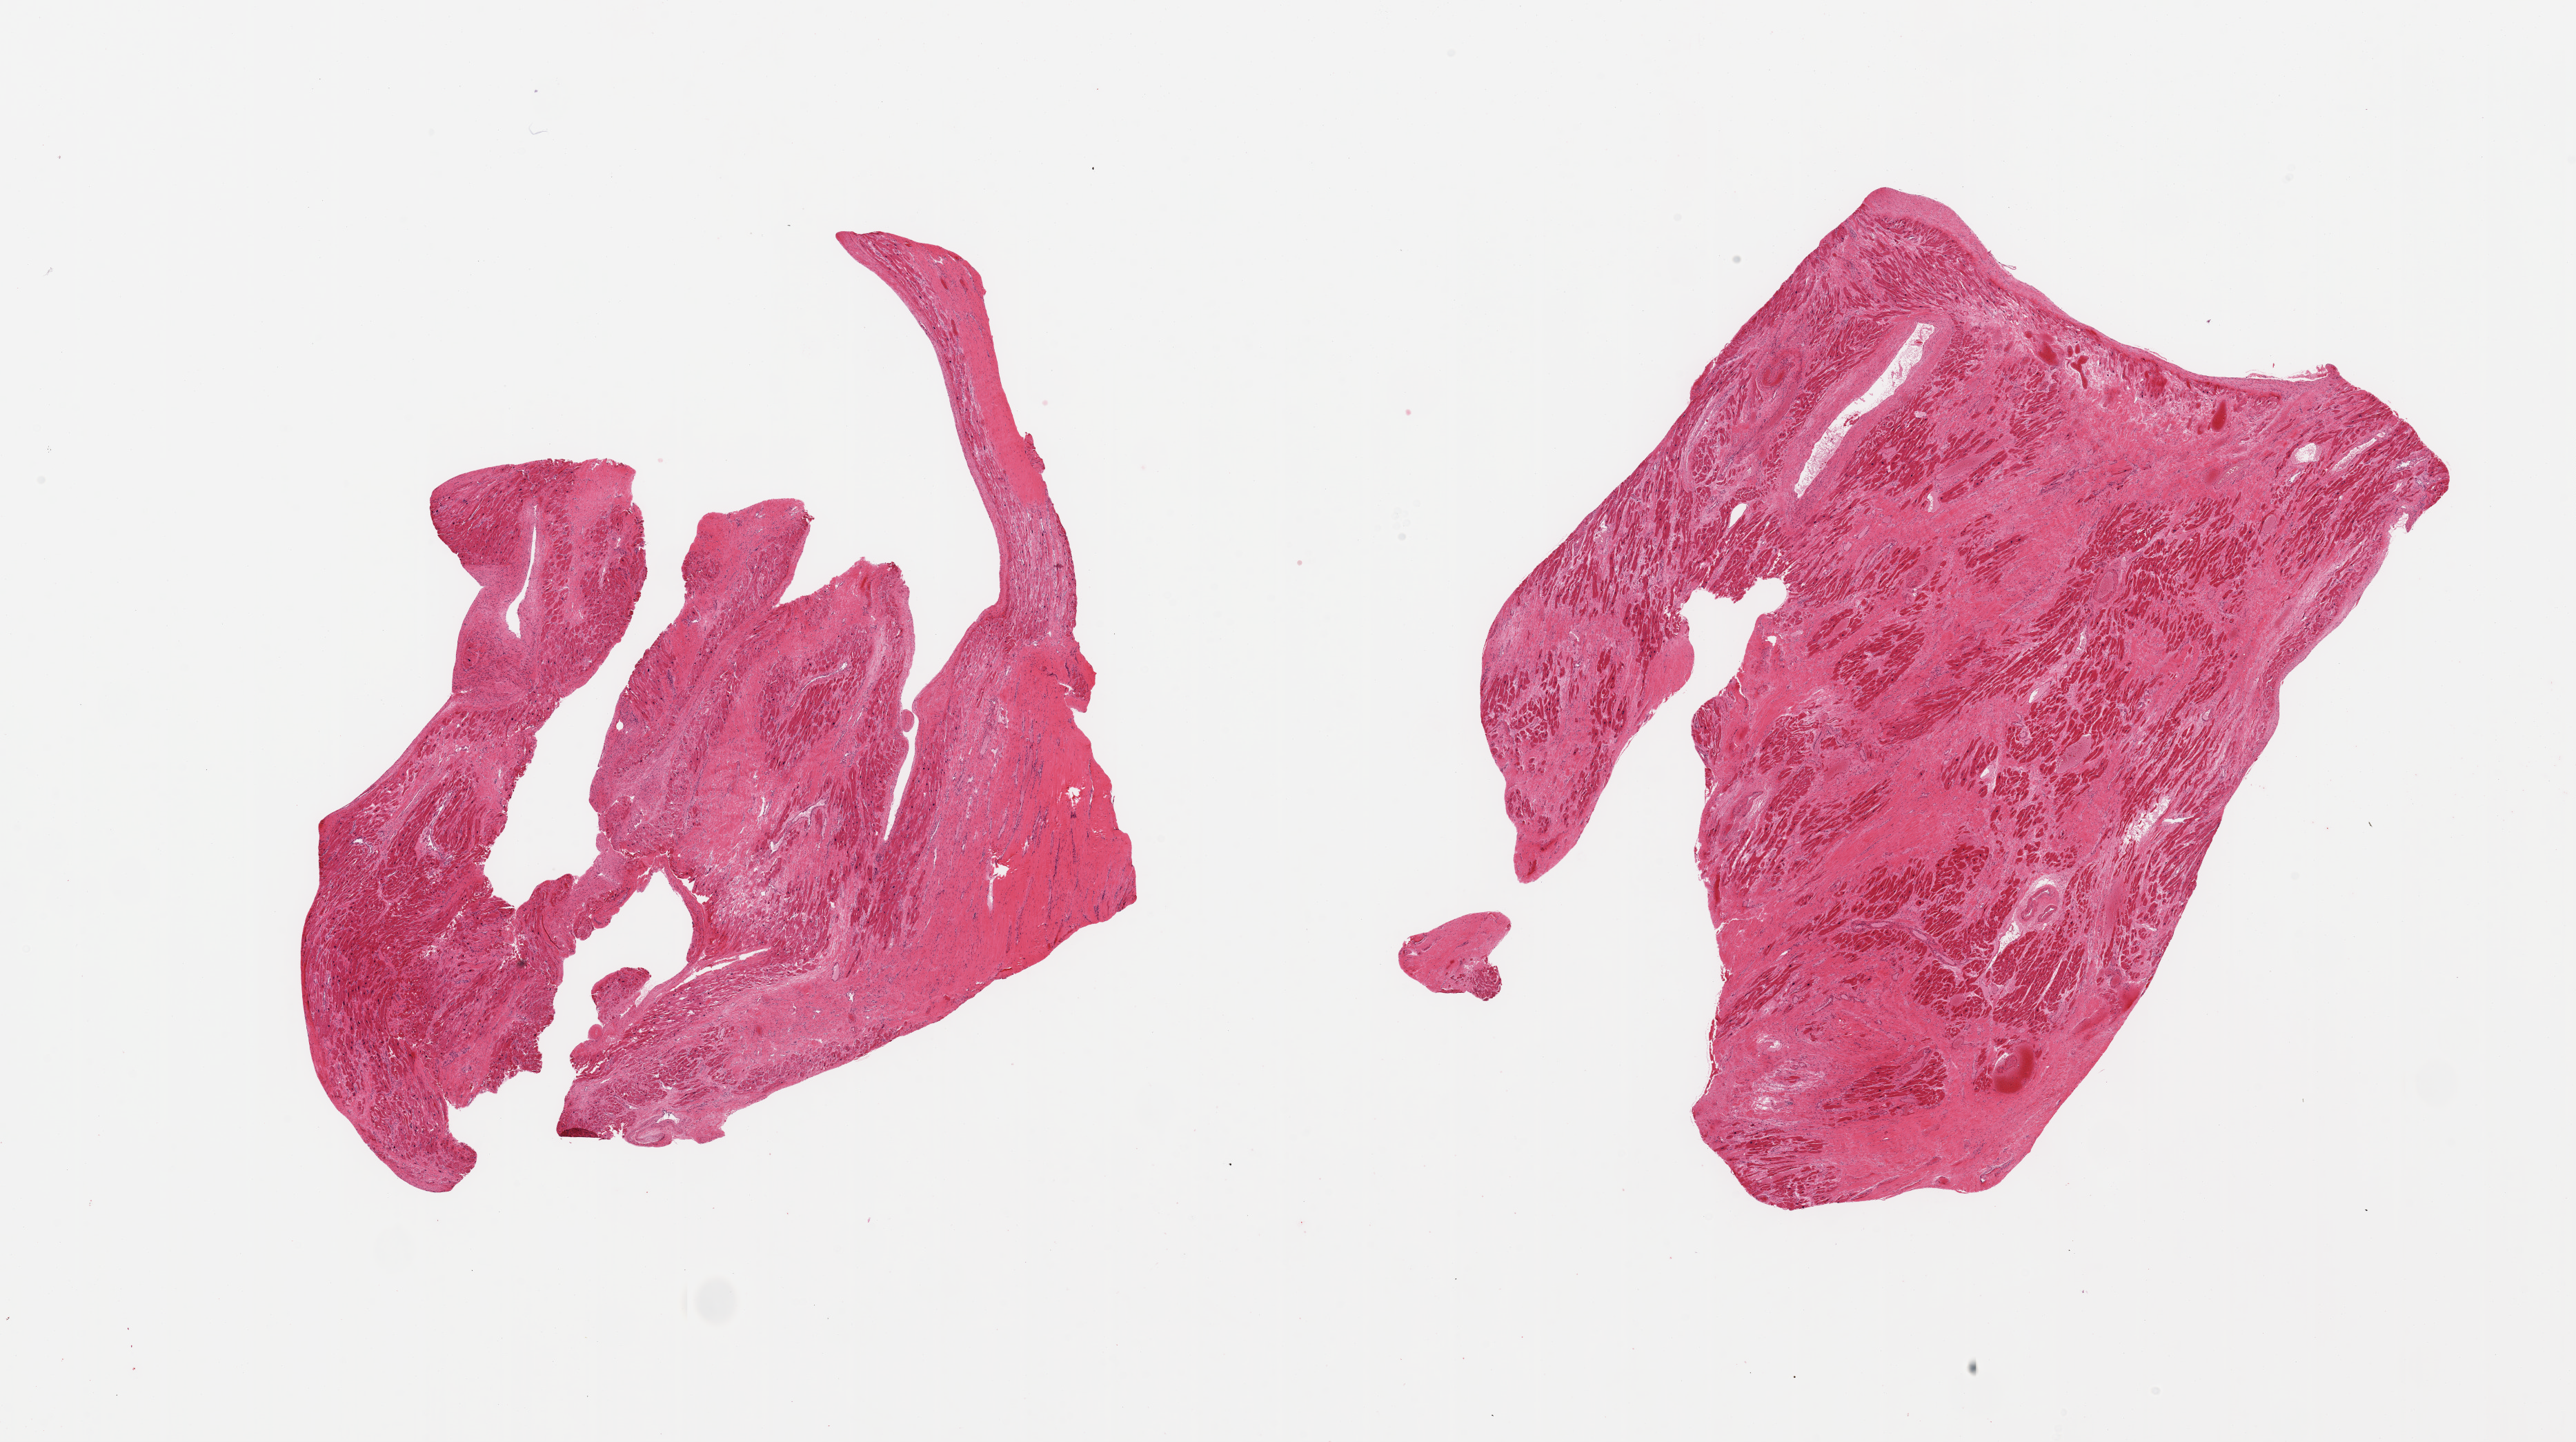
Hematoxylin and eosin (H&E) whole-slide image, brightfield, a low-resolution overview of the entire scanned area, about 29.5 x 16.5 mm (from a 20x scan); PAXgene-fixed paraffin-embedded (PFPE) section; sampled site (target tissue): heart; tissue donor sample. Donor: male.
• reviewer comment on this tissue sample: 2 pieces; extensively scarred (>50%) myocardium consistent with old infarcts